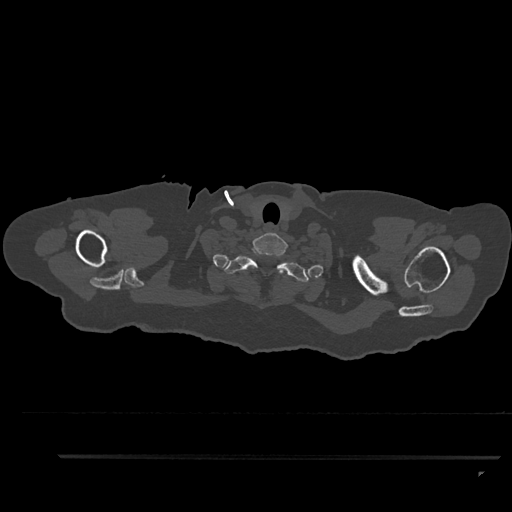
CT including the spine, one axial slice; slice 775 of 797 in the series (ordered by position); 120 kVp; bone window (W 1800 / L 400 HU); 0.5 mm slice thickness; 512 × 512 image matrix, field of view 408 × 408 mm. Female patient, age 44 years. Case-level facts recorded for this patient, not image findings: primary cancer: renal; vertebrae with lytic lesions (as recorded): L1.
Structures marked on this image (semi-automatic segmentation, software-assisted and operator-edited):
- T1 vertebra: bounding box (x1, y1, x2, y2) in pixels: (224, 246, 309, 282)